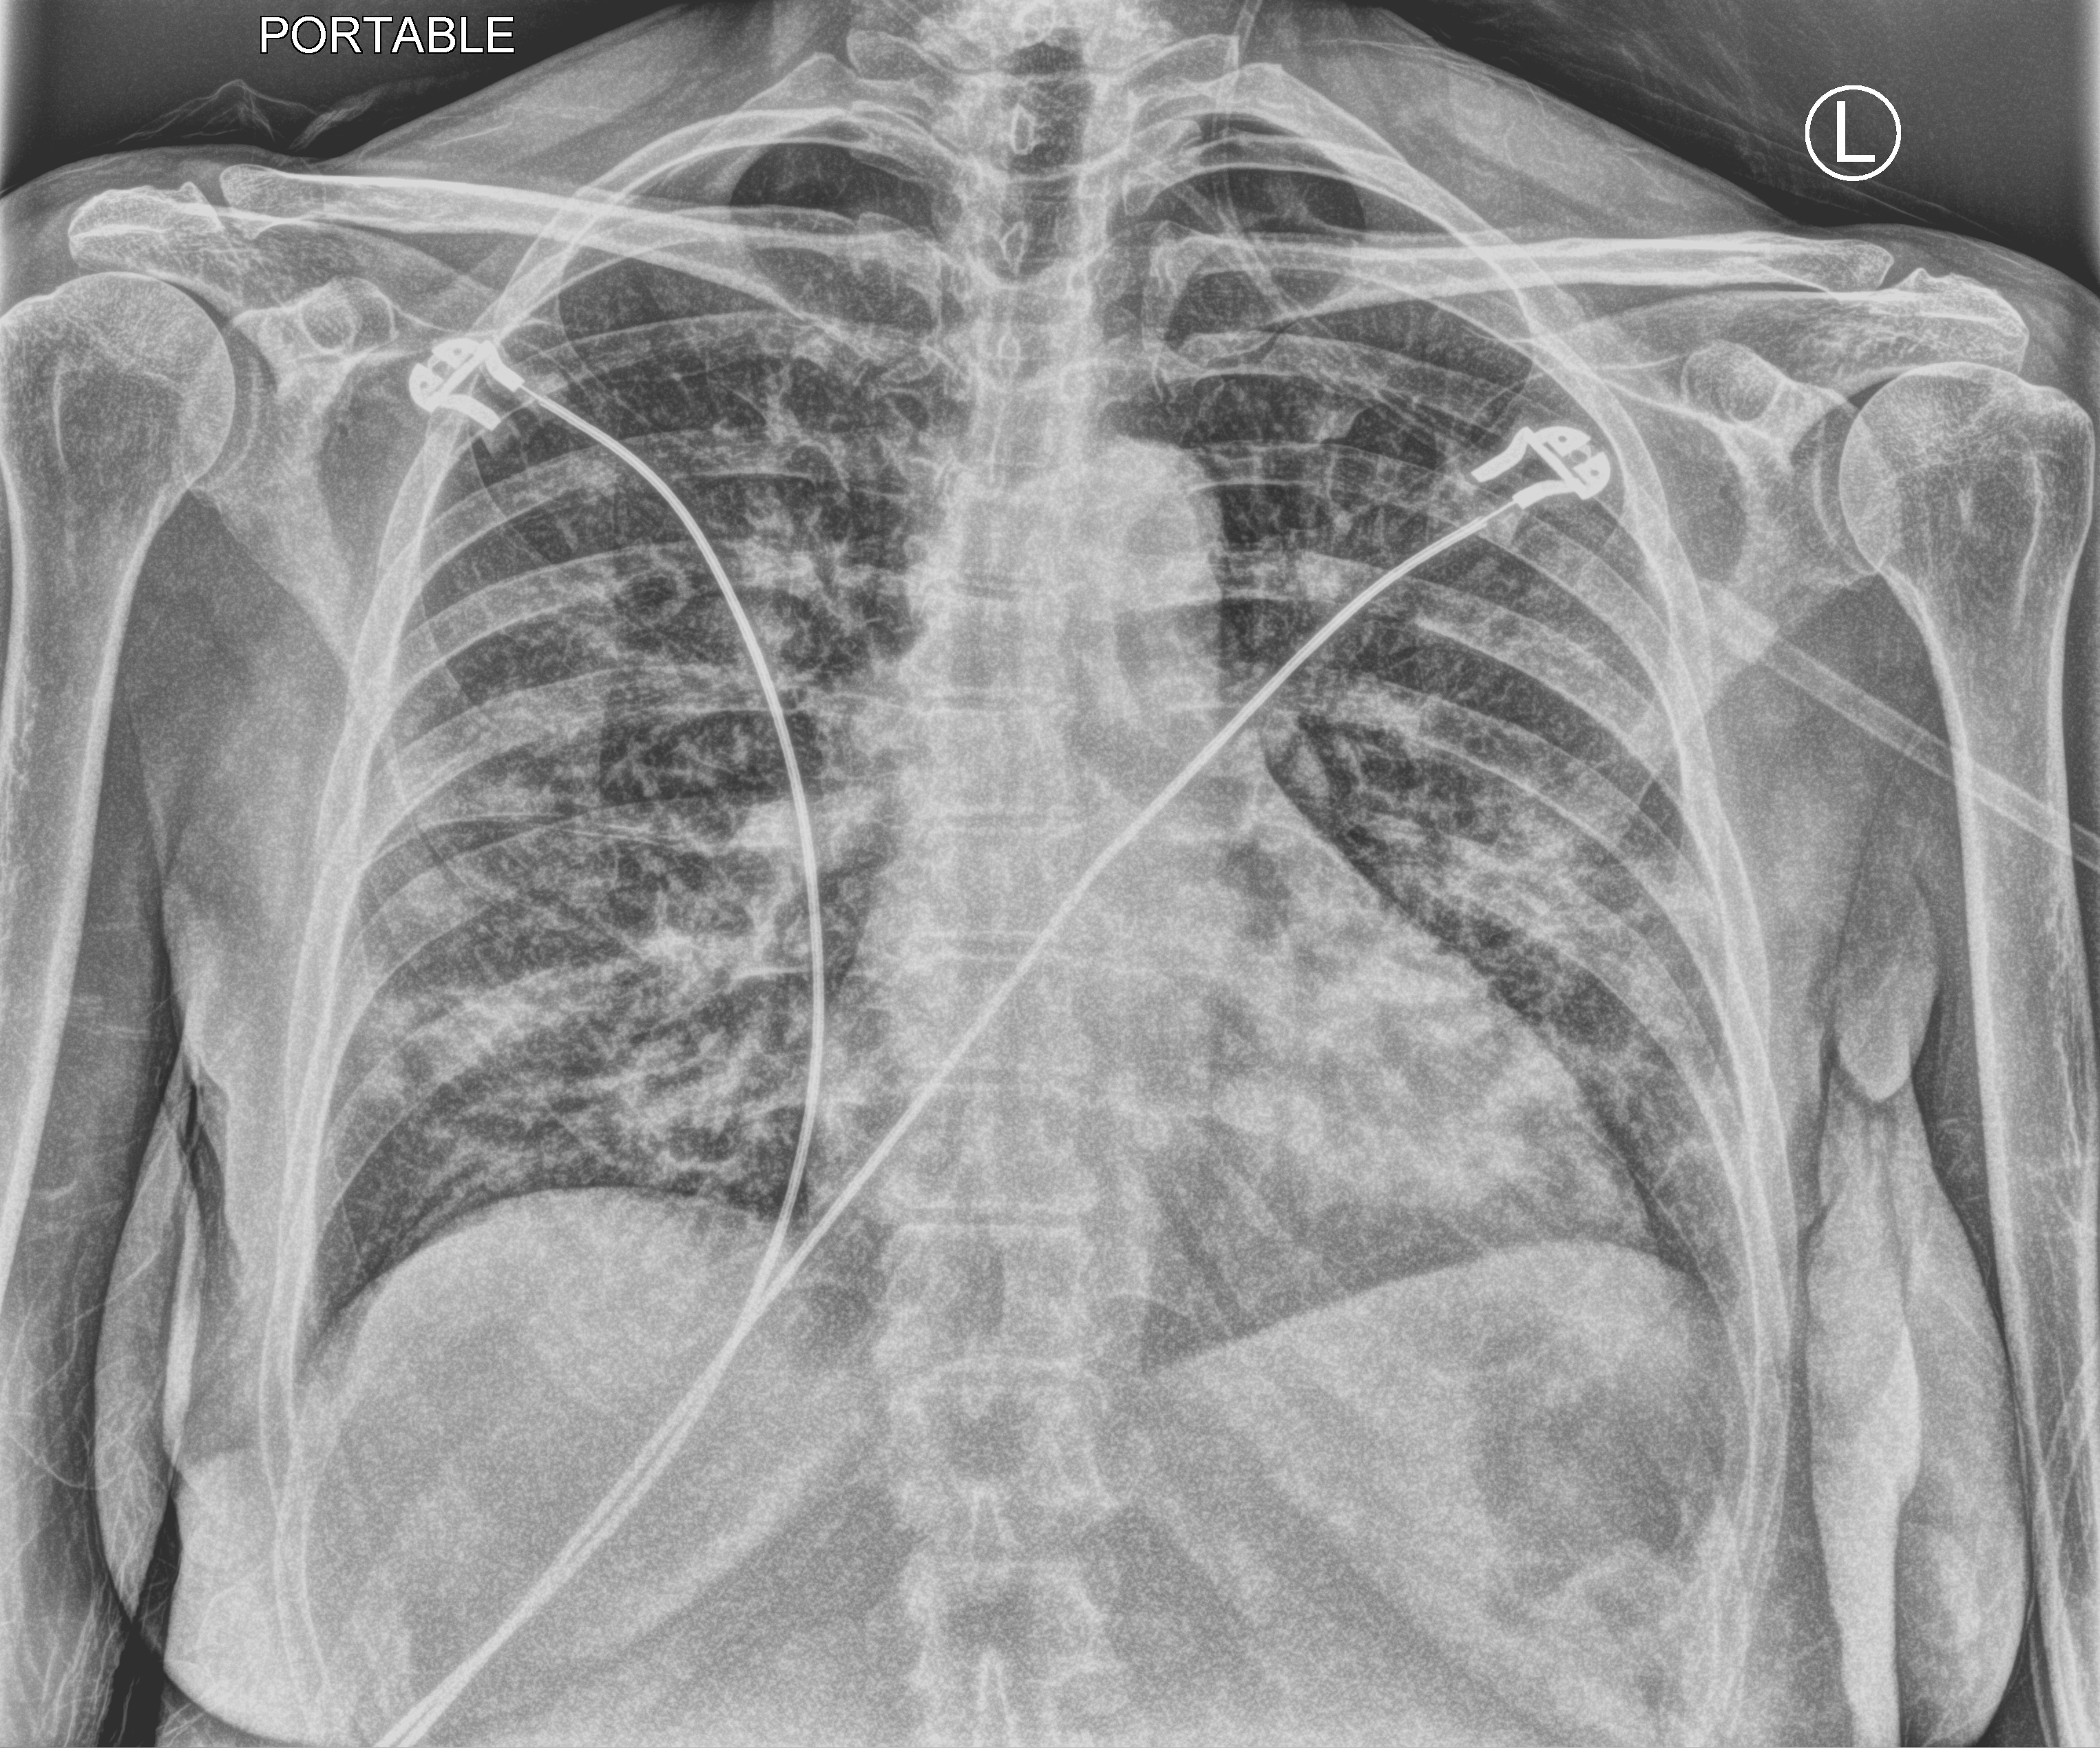
Bedside chest radiograph (computed radiography); anteroposterior (AP) projection. Patient hospitalised with COVID-19; female, aged 18–59 years.
Hospital-stay facts (about this admission, not read from this image; timing relative to this image not recorded): admitted to intensive care during this hospital stay: no; mechanically ventilated during this hospital stay: no.